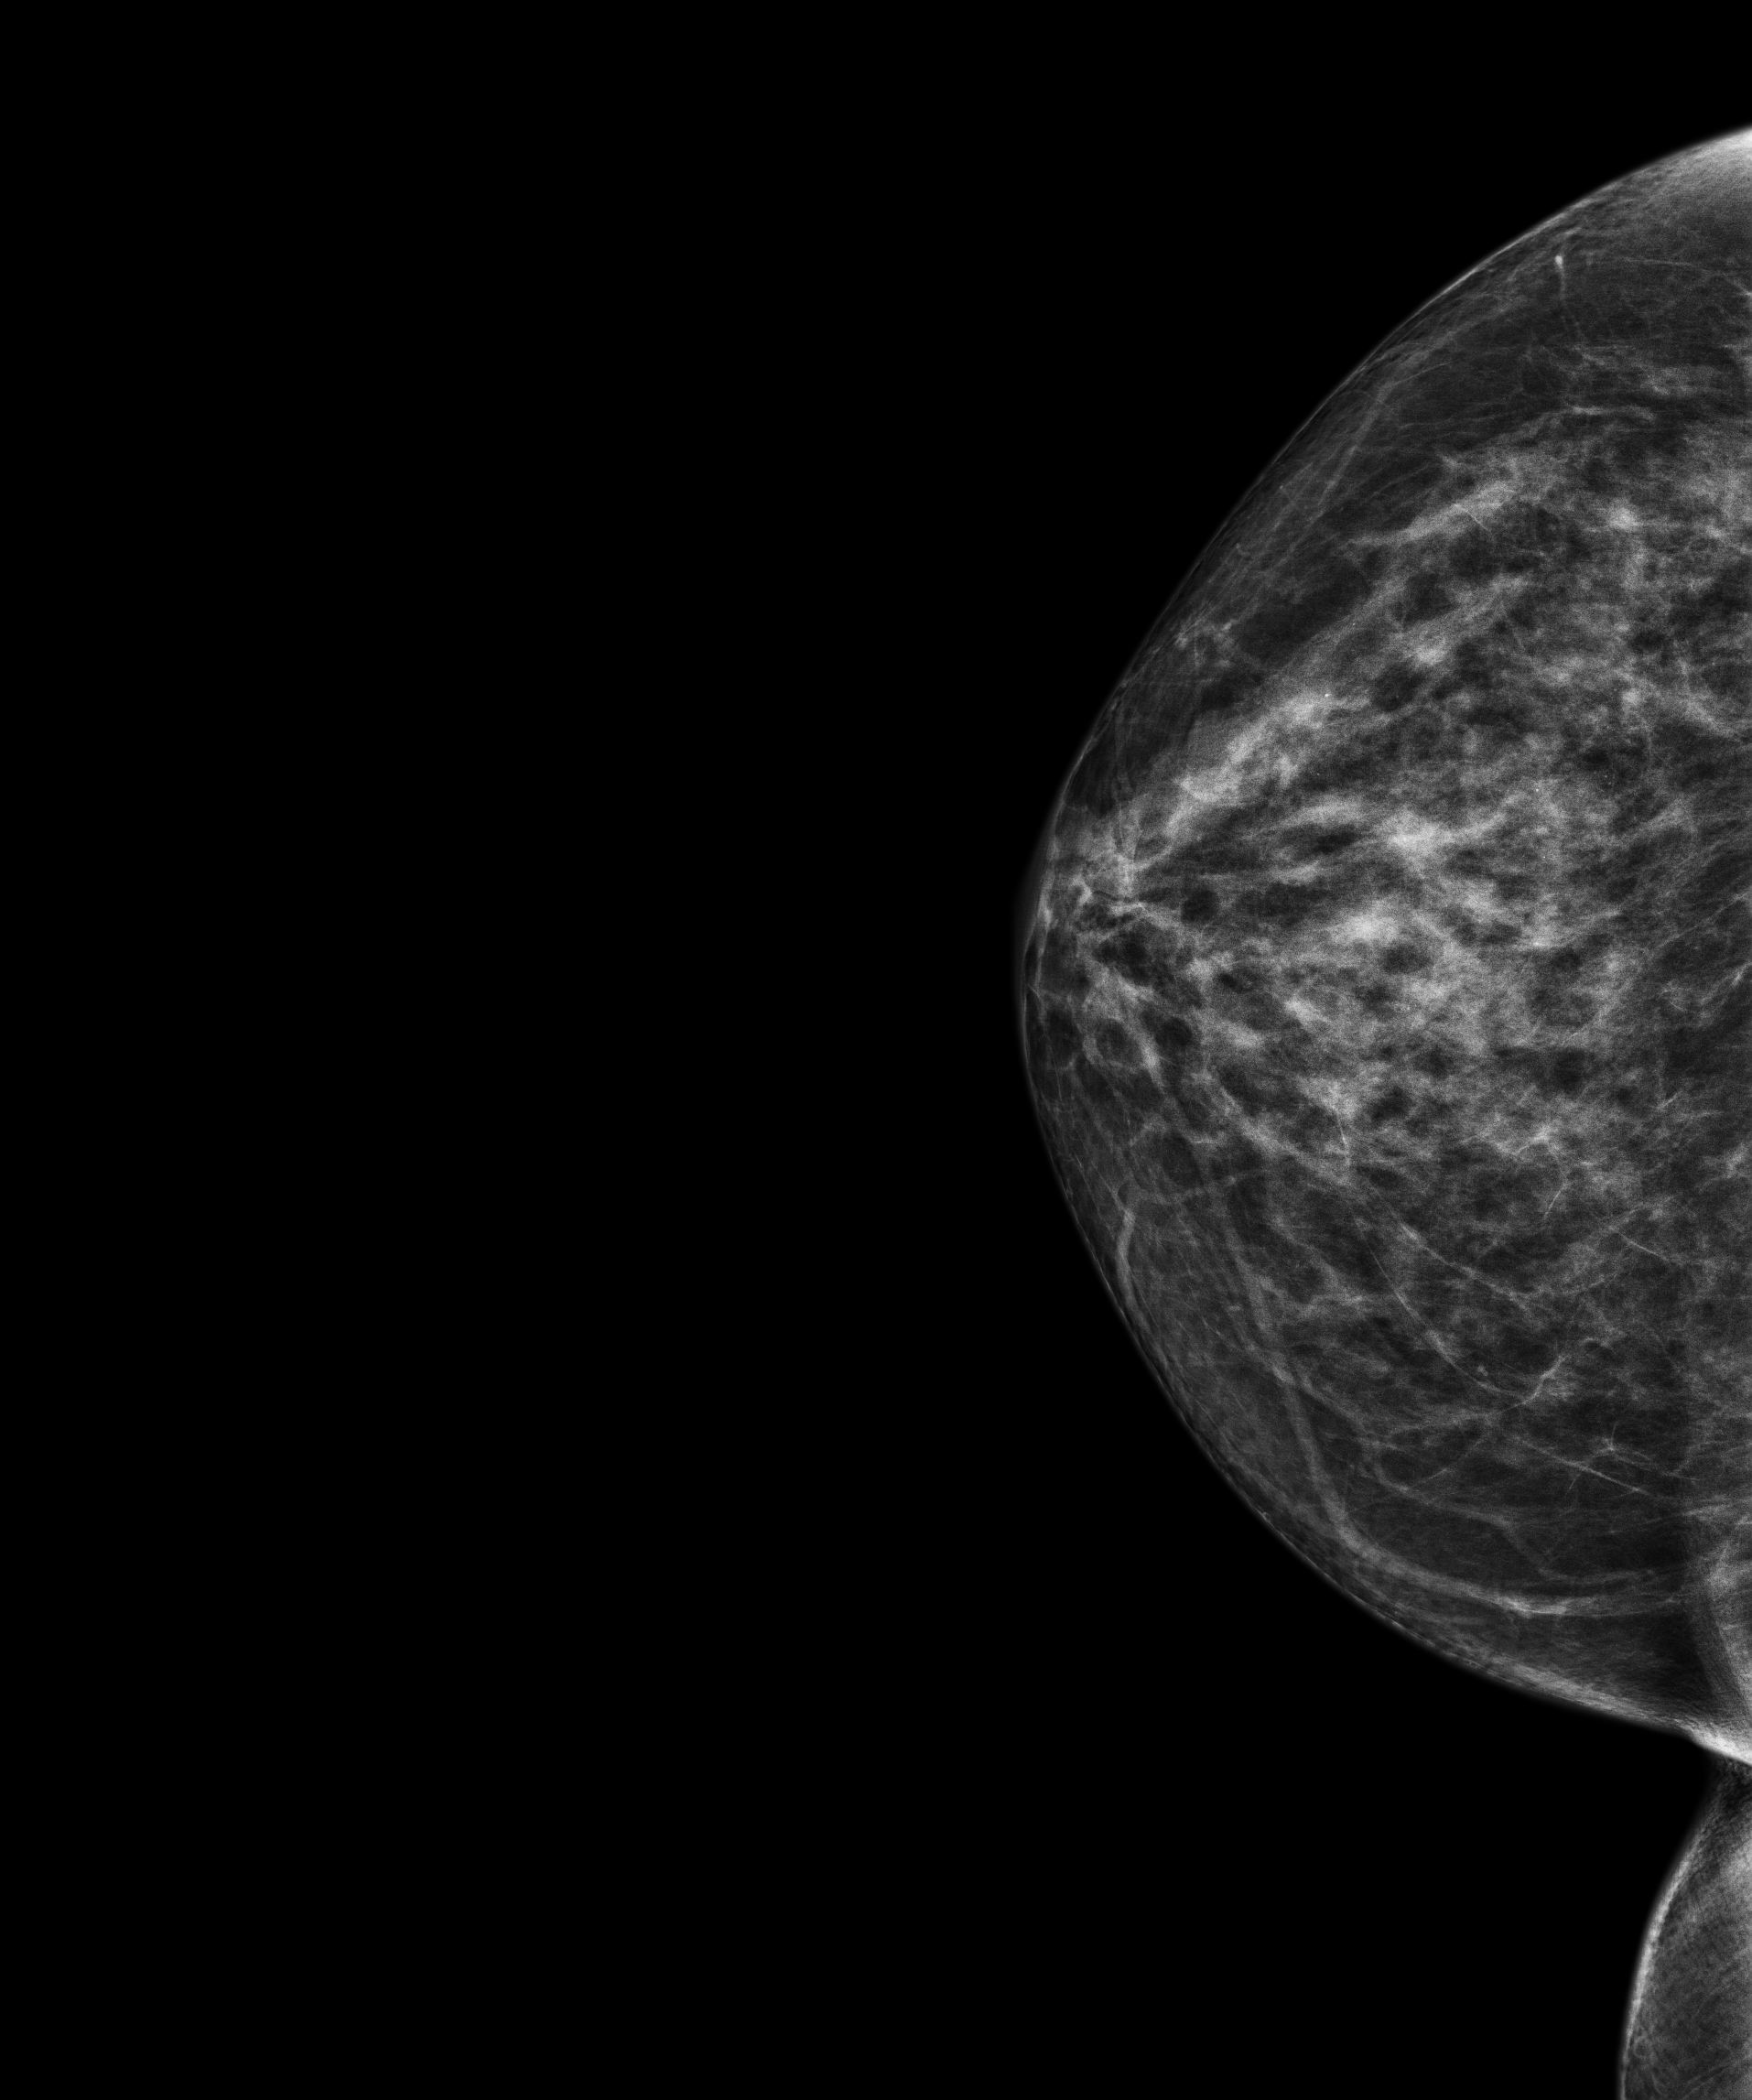
Annual screening mammography examination. Female patient, age 59 years.
Image type: full-field digital mammogram. Breast: right. Projection: craniocaudal (CC) view.